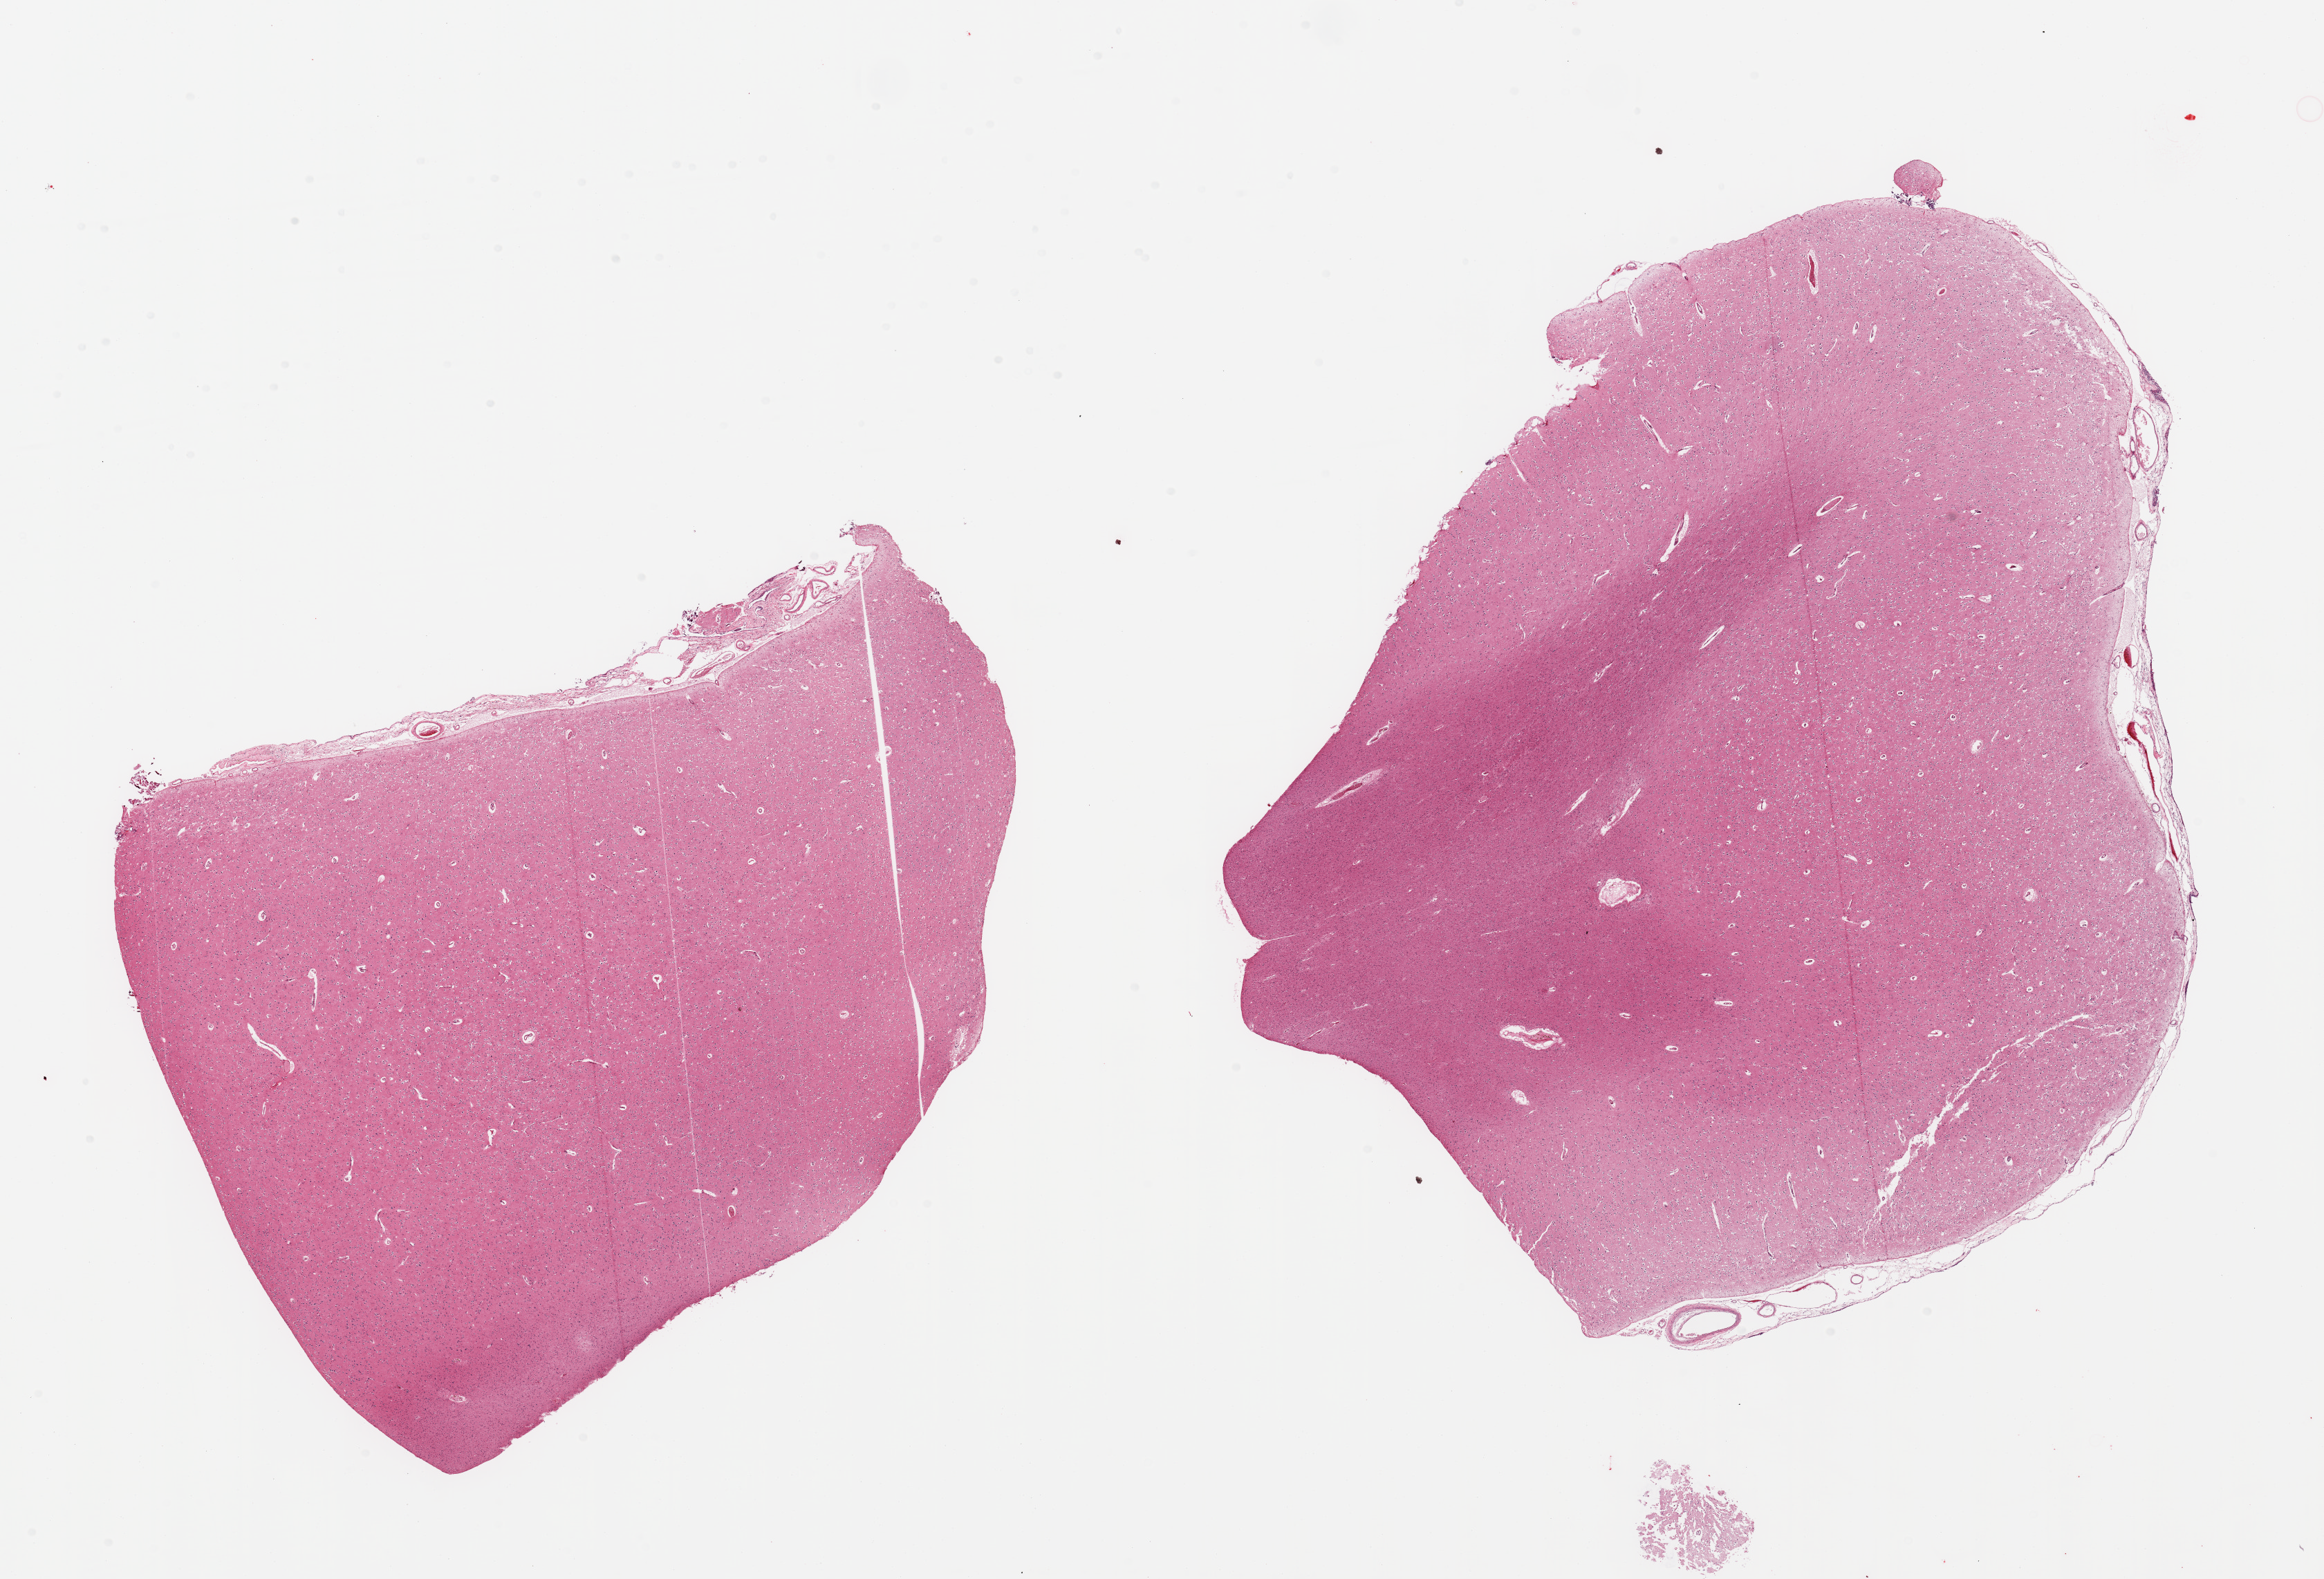
Digitized H&E-stained section, brightfield — whole scanned area (about 26.6 x 18.1 mm, acquisition: 20x scan) shown as a low-resolution overview; PAXgene-fixed, paraffin-embedded tissue; sampled site (target tissue): cerebral cortex; tissue donor sample. Female donor.
* reviewer comment on this tissue sample: 2 pieces; cerebrum with thin layer of meninges